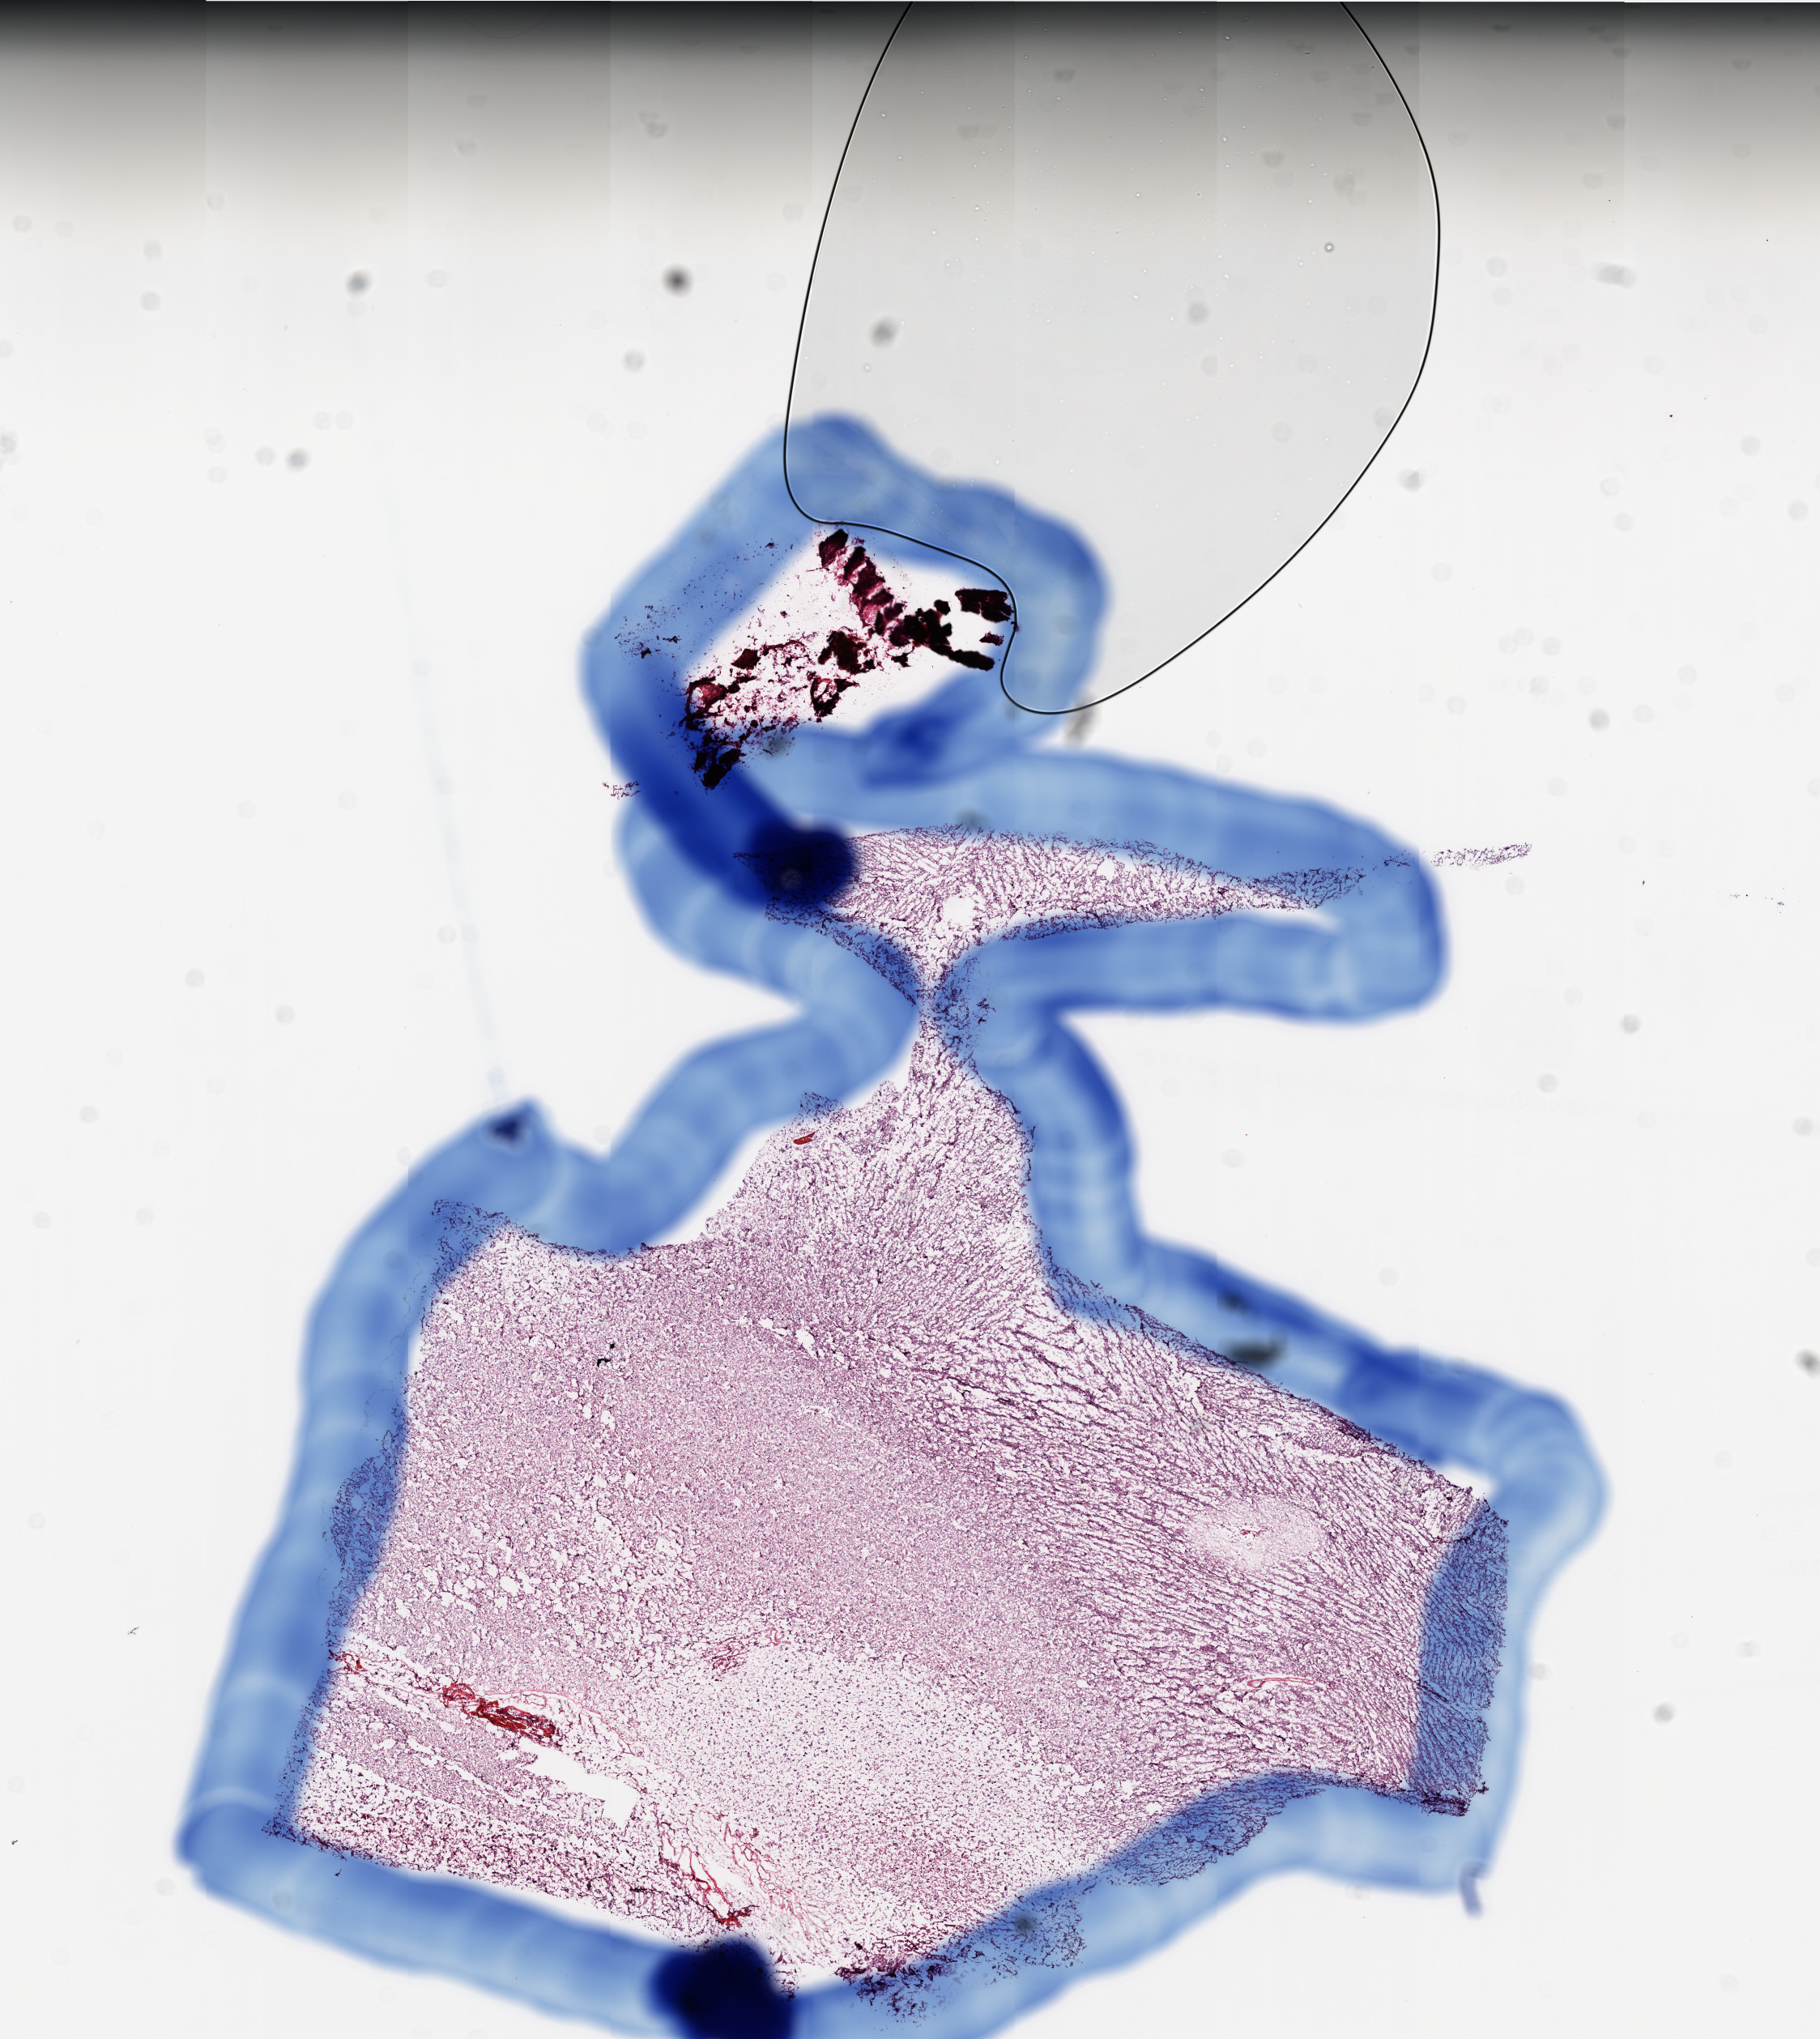
Digitized H&E tissue section (whole slide) — shown as a low-resolution overview of the whole scanned area (about 9.0 x 10.1 mm, from a 20x scan). Frozen section from the top of the tissue portion. Primary tumour sample from the brain. Female, age 56 years at initial diagnosis. Slide review estimates, as recorded: tumour cells 0%, tumour nuclei 0%, normal cells 100%, stromal cells 0%, necrosis 0%.
• diagnosis: Glioblastoma